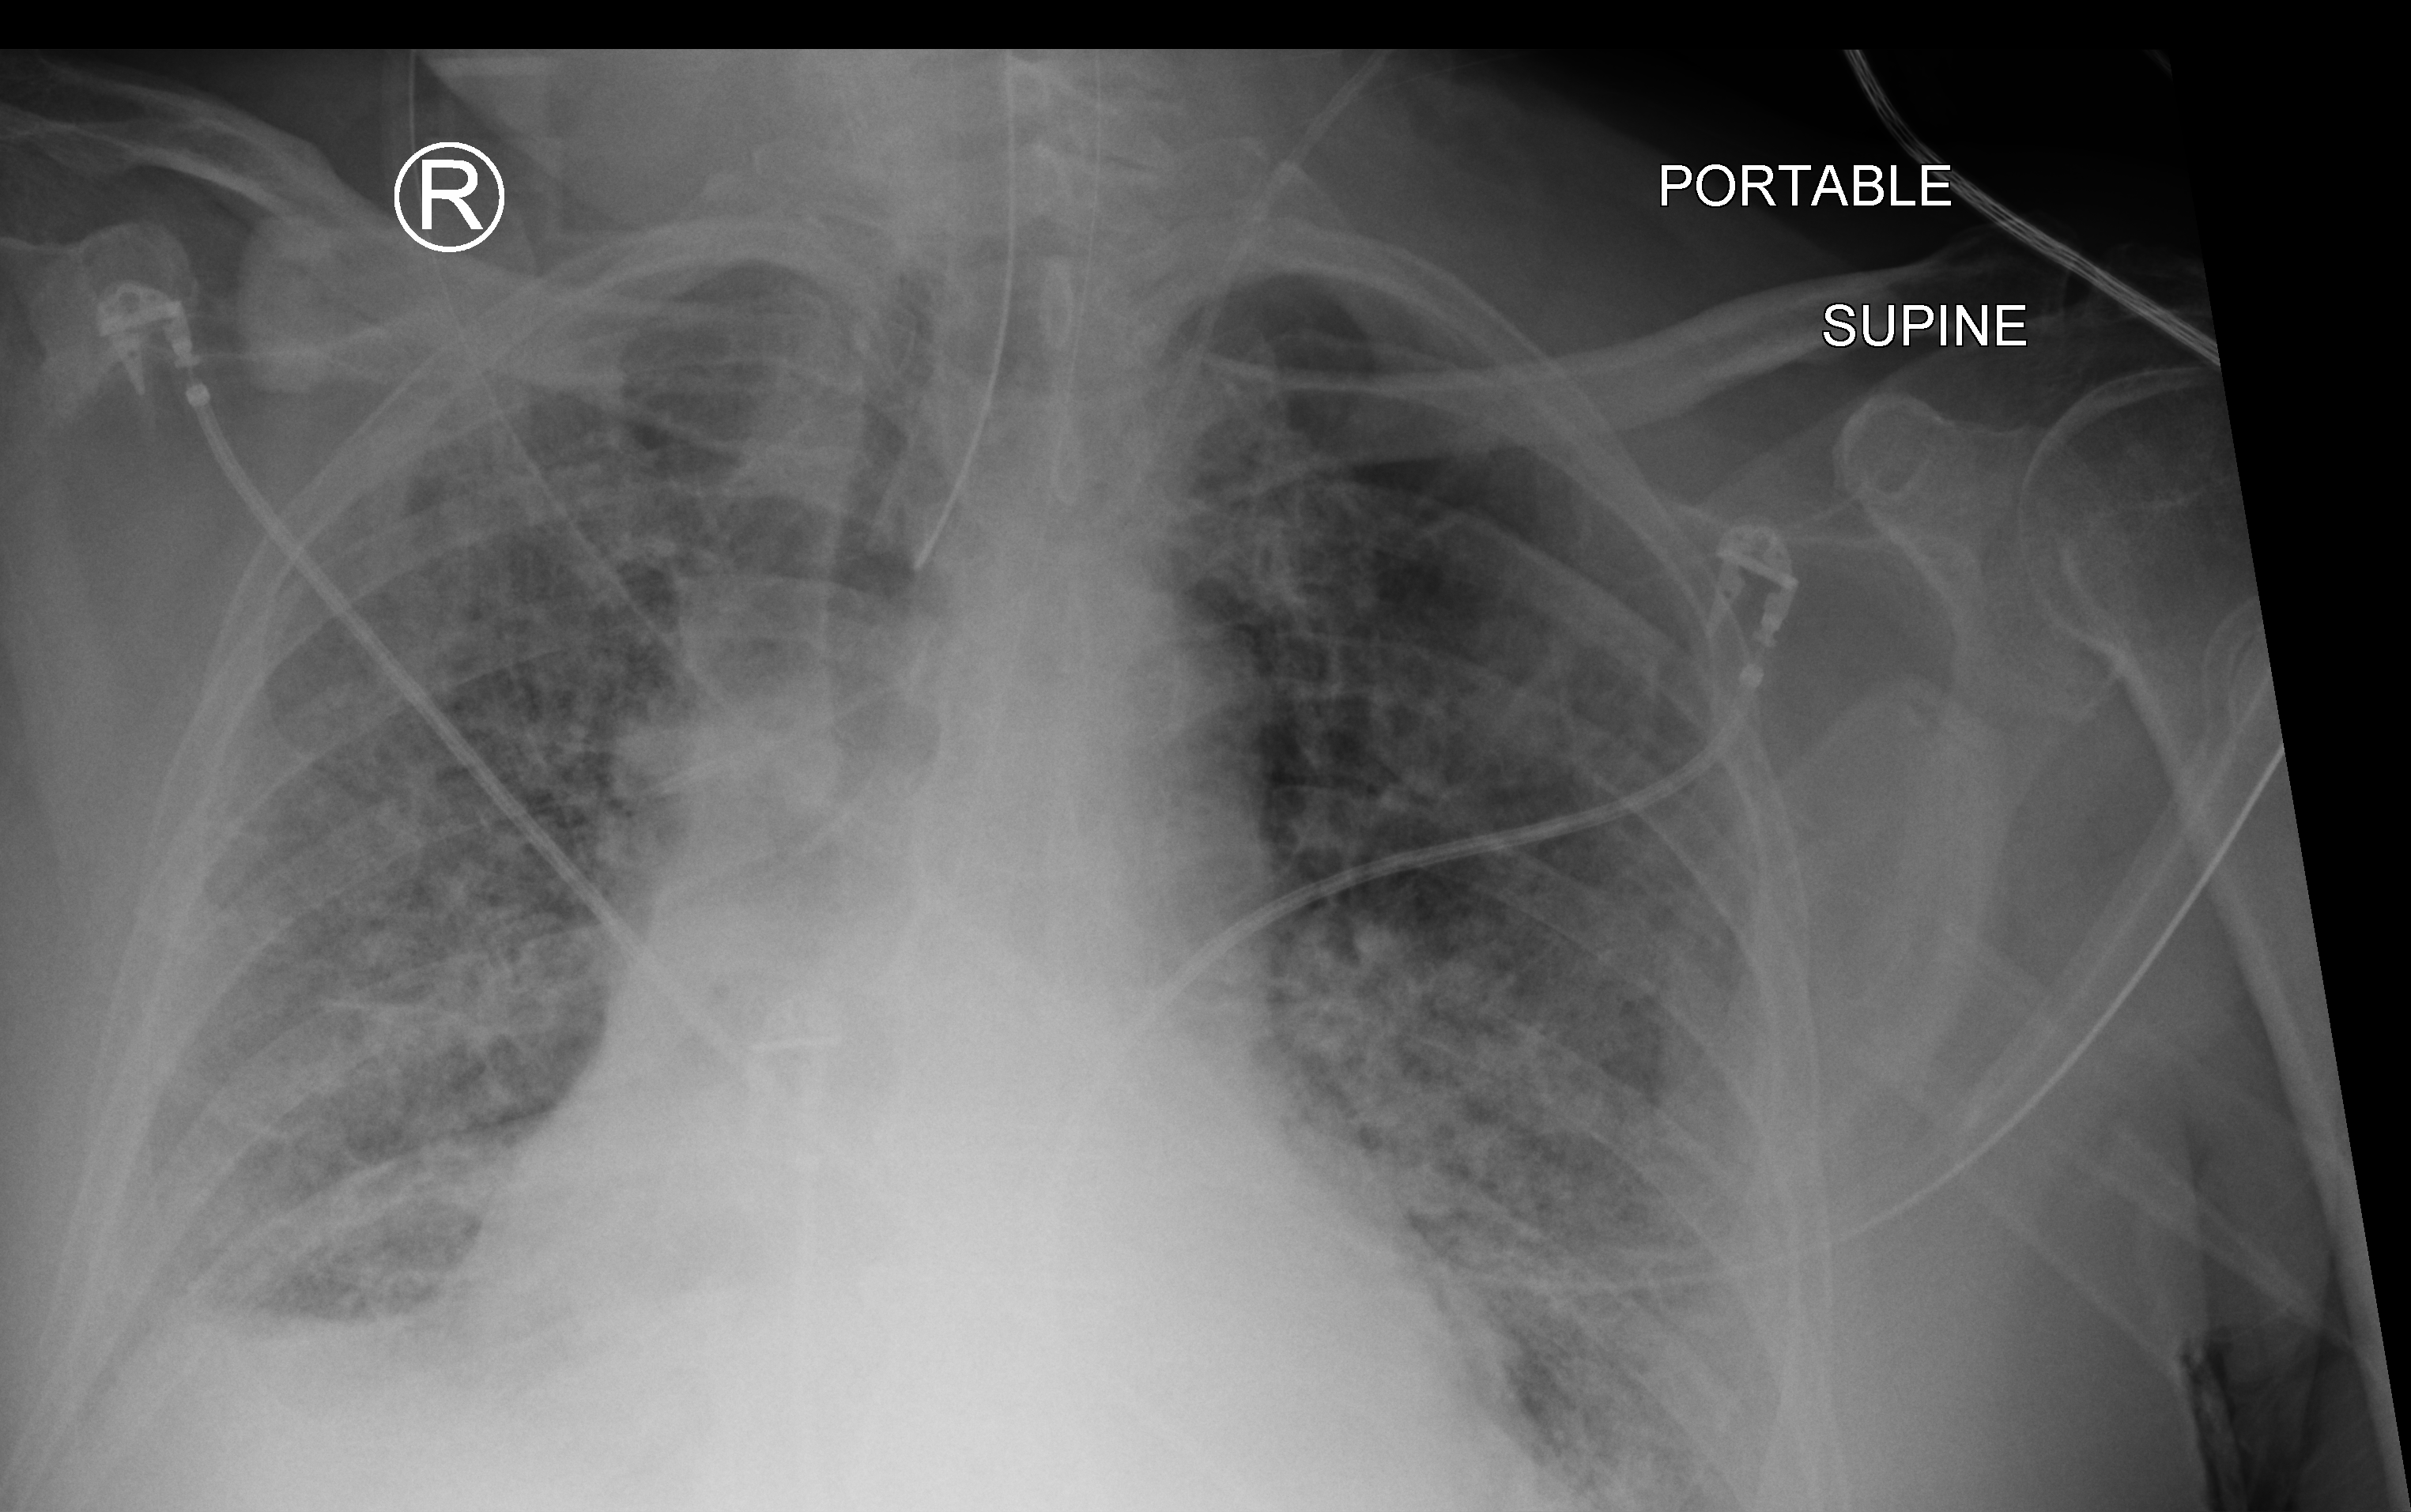
Chest X-ray (portable); anteroposterior (AP) projection. Male patient hospitalised with COVID-19, age 75–90 years.
Admission-level facts for this patient (not findings on this image; timing relative to this image not recorded): length of hospital stay: 14 days; hypertension (admission record): yes.